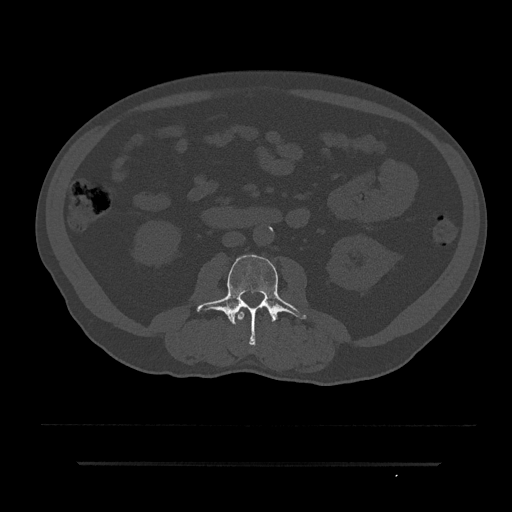
CT including the spine, one axial slice; slice 14 of 797 in the series (ordered by position); reconstruction kernel Br40s/3; 120 kVp; bone window (W 1800 / L 400 HU); 512 × 512 image matrix. Patient: male, 59 years. Case-level facts recorded for this patient, not image findings: primary cancer: bile ducts; vertebrae with lytic lesions (as recorded): T10.
Structures marked on this image (semi-automatically segmented with operator editing):
- L2 vertebra: box from (x=234, y=309) to (x=267, y=321) px
- L3 vertebra: (x=196, y=254)–(x=307, y=345)